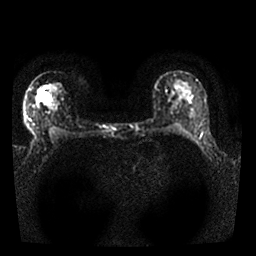
Breast MRI, one axial slice. Position 17 of 25 along the scan axis. Diffusion-weighted series; image 2 of 4 stored at this slice position (different b-values; order by instance number). 1.5 T. 4 mm slice thickness. 256 × 256 image matrix. Female patient.
Structures marked on this image (outlined manually by an expert reader):
- tumour on diffusion-weighted imaging: bounding box (x1, y1, x2, y2) in pixels: (44, 94, 48, 98)